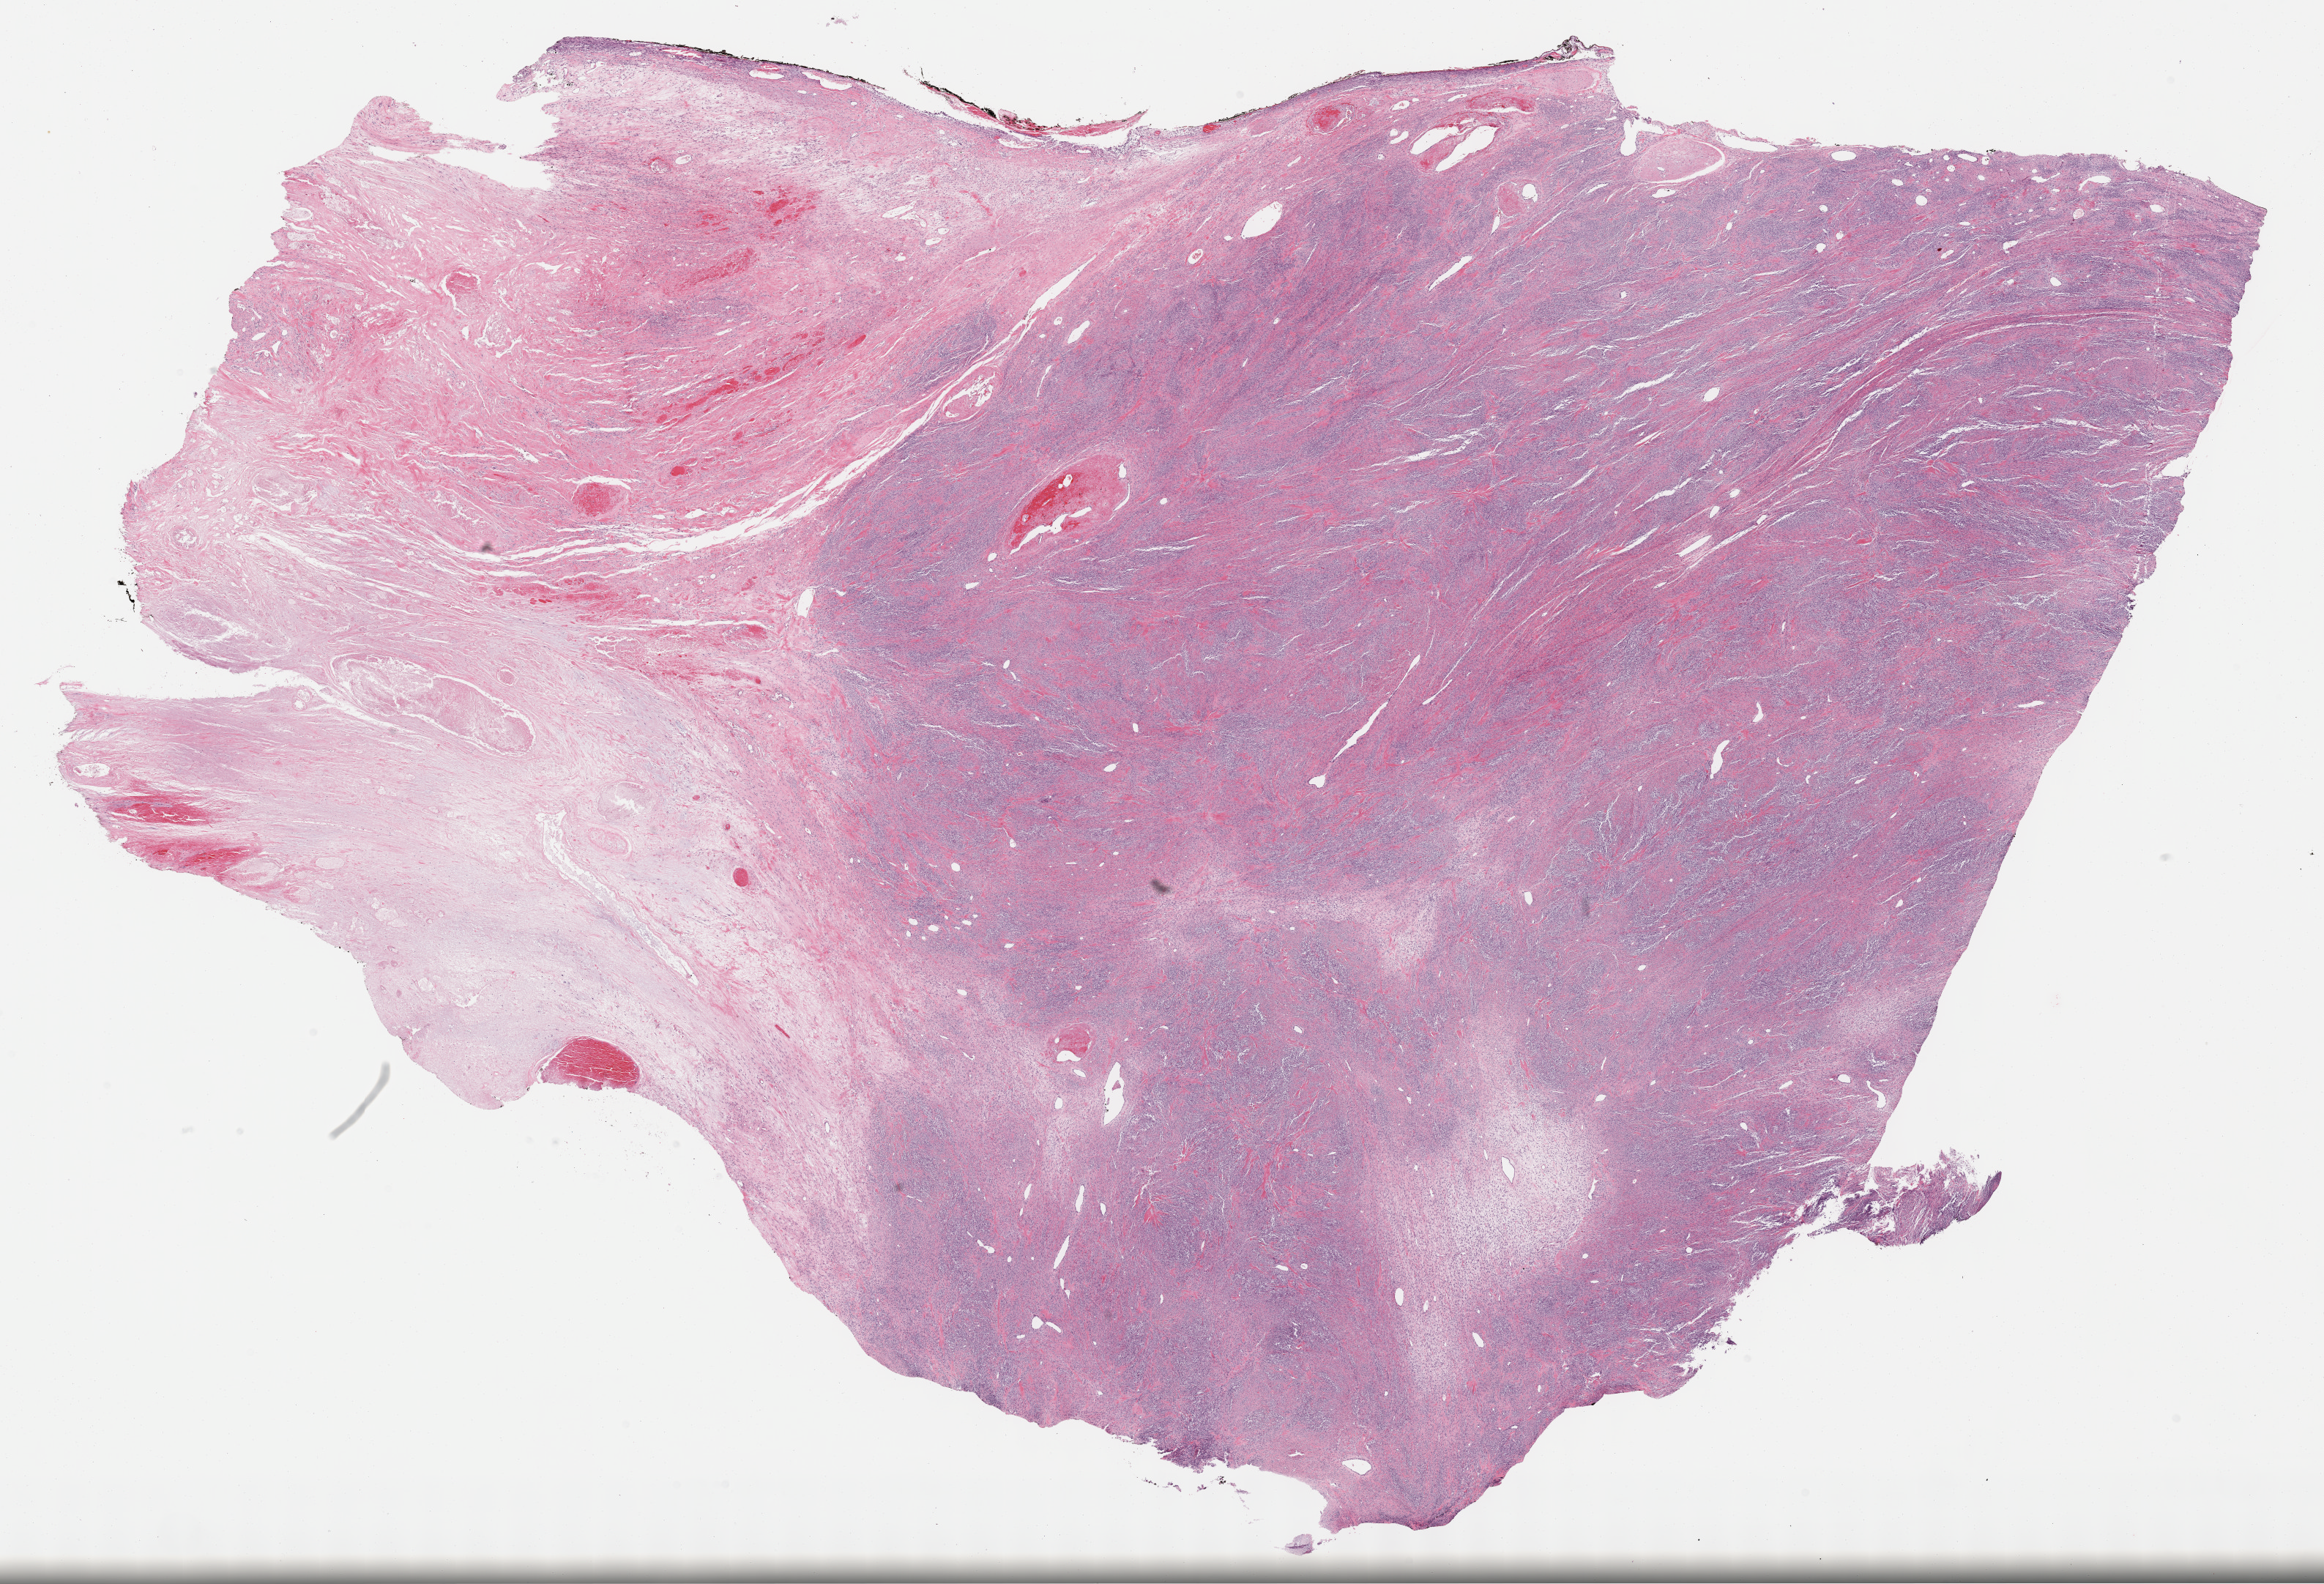
Whole-slide histology image, H&E-stained — whole scanned area (about 25.7 x 17.5 mm, slide scanned at 40x) shown as a low-resolution overview; formalin-fixed paraffin-embedded (FFPE) diagnostic section; sample: primary tumour, retroperitoneum and peritoneum. Female, age 71 years at initial diagnosis.
Diagnosis: Undifferentiated sarcoma (retroperitoneum).